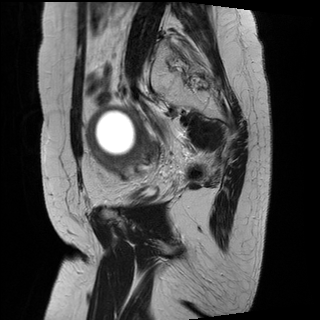
Pelvic MRI for cervical cancer, one sagittal slice; position 23 of 29 along the scan axis; T2-weighted; 1.5 T; TE 89 ms, TR 2930 ms; 4 mm slice thickness; 320 × 320 image matrix, field of view 260 × 260 mm. Female patient, age 49 years.
Annotated regions visible in this slice (expert manual segmentation):
- uterus and cervix: bounding box (x1, y1, x2, y2) in pixels: (87, 106, 148, 173)